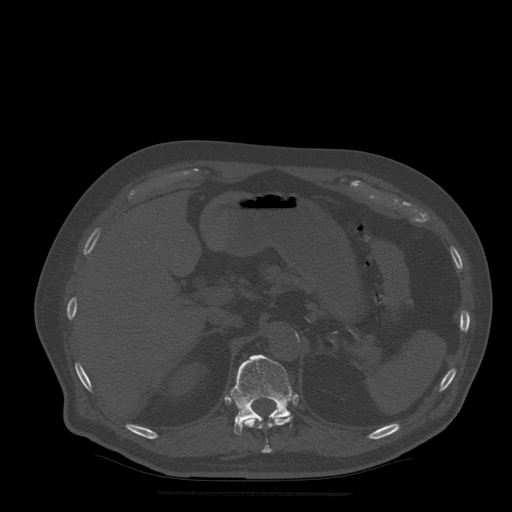
CT including the spine, one axial slice. Position 229 of 522 along the scan axis. Bone window (W 1800 / L 400 HU). 1.25 mm slice thickness. 512 × 512 image matrix, field of view 420 × 420 mm. Patient age 72 years. From the clinical record (not read from this slice): primary cancer: prostate.
Annotated regions visible in this slice (semi-automatically segmented with operator editing):
- T11 vertebra: box from (x=234, y=414) to (x=293, y=453) px
- T12 vertebra: (x=231, y=355)–(x=293, y=435)